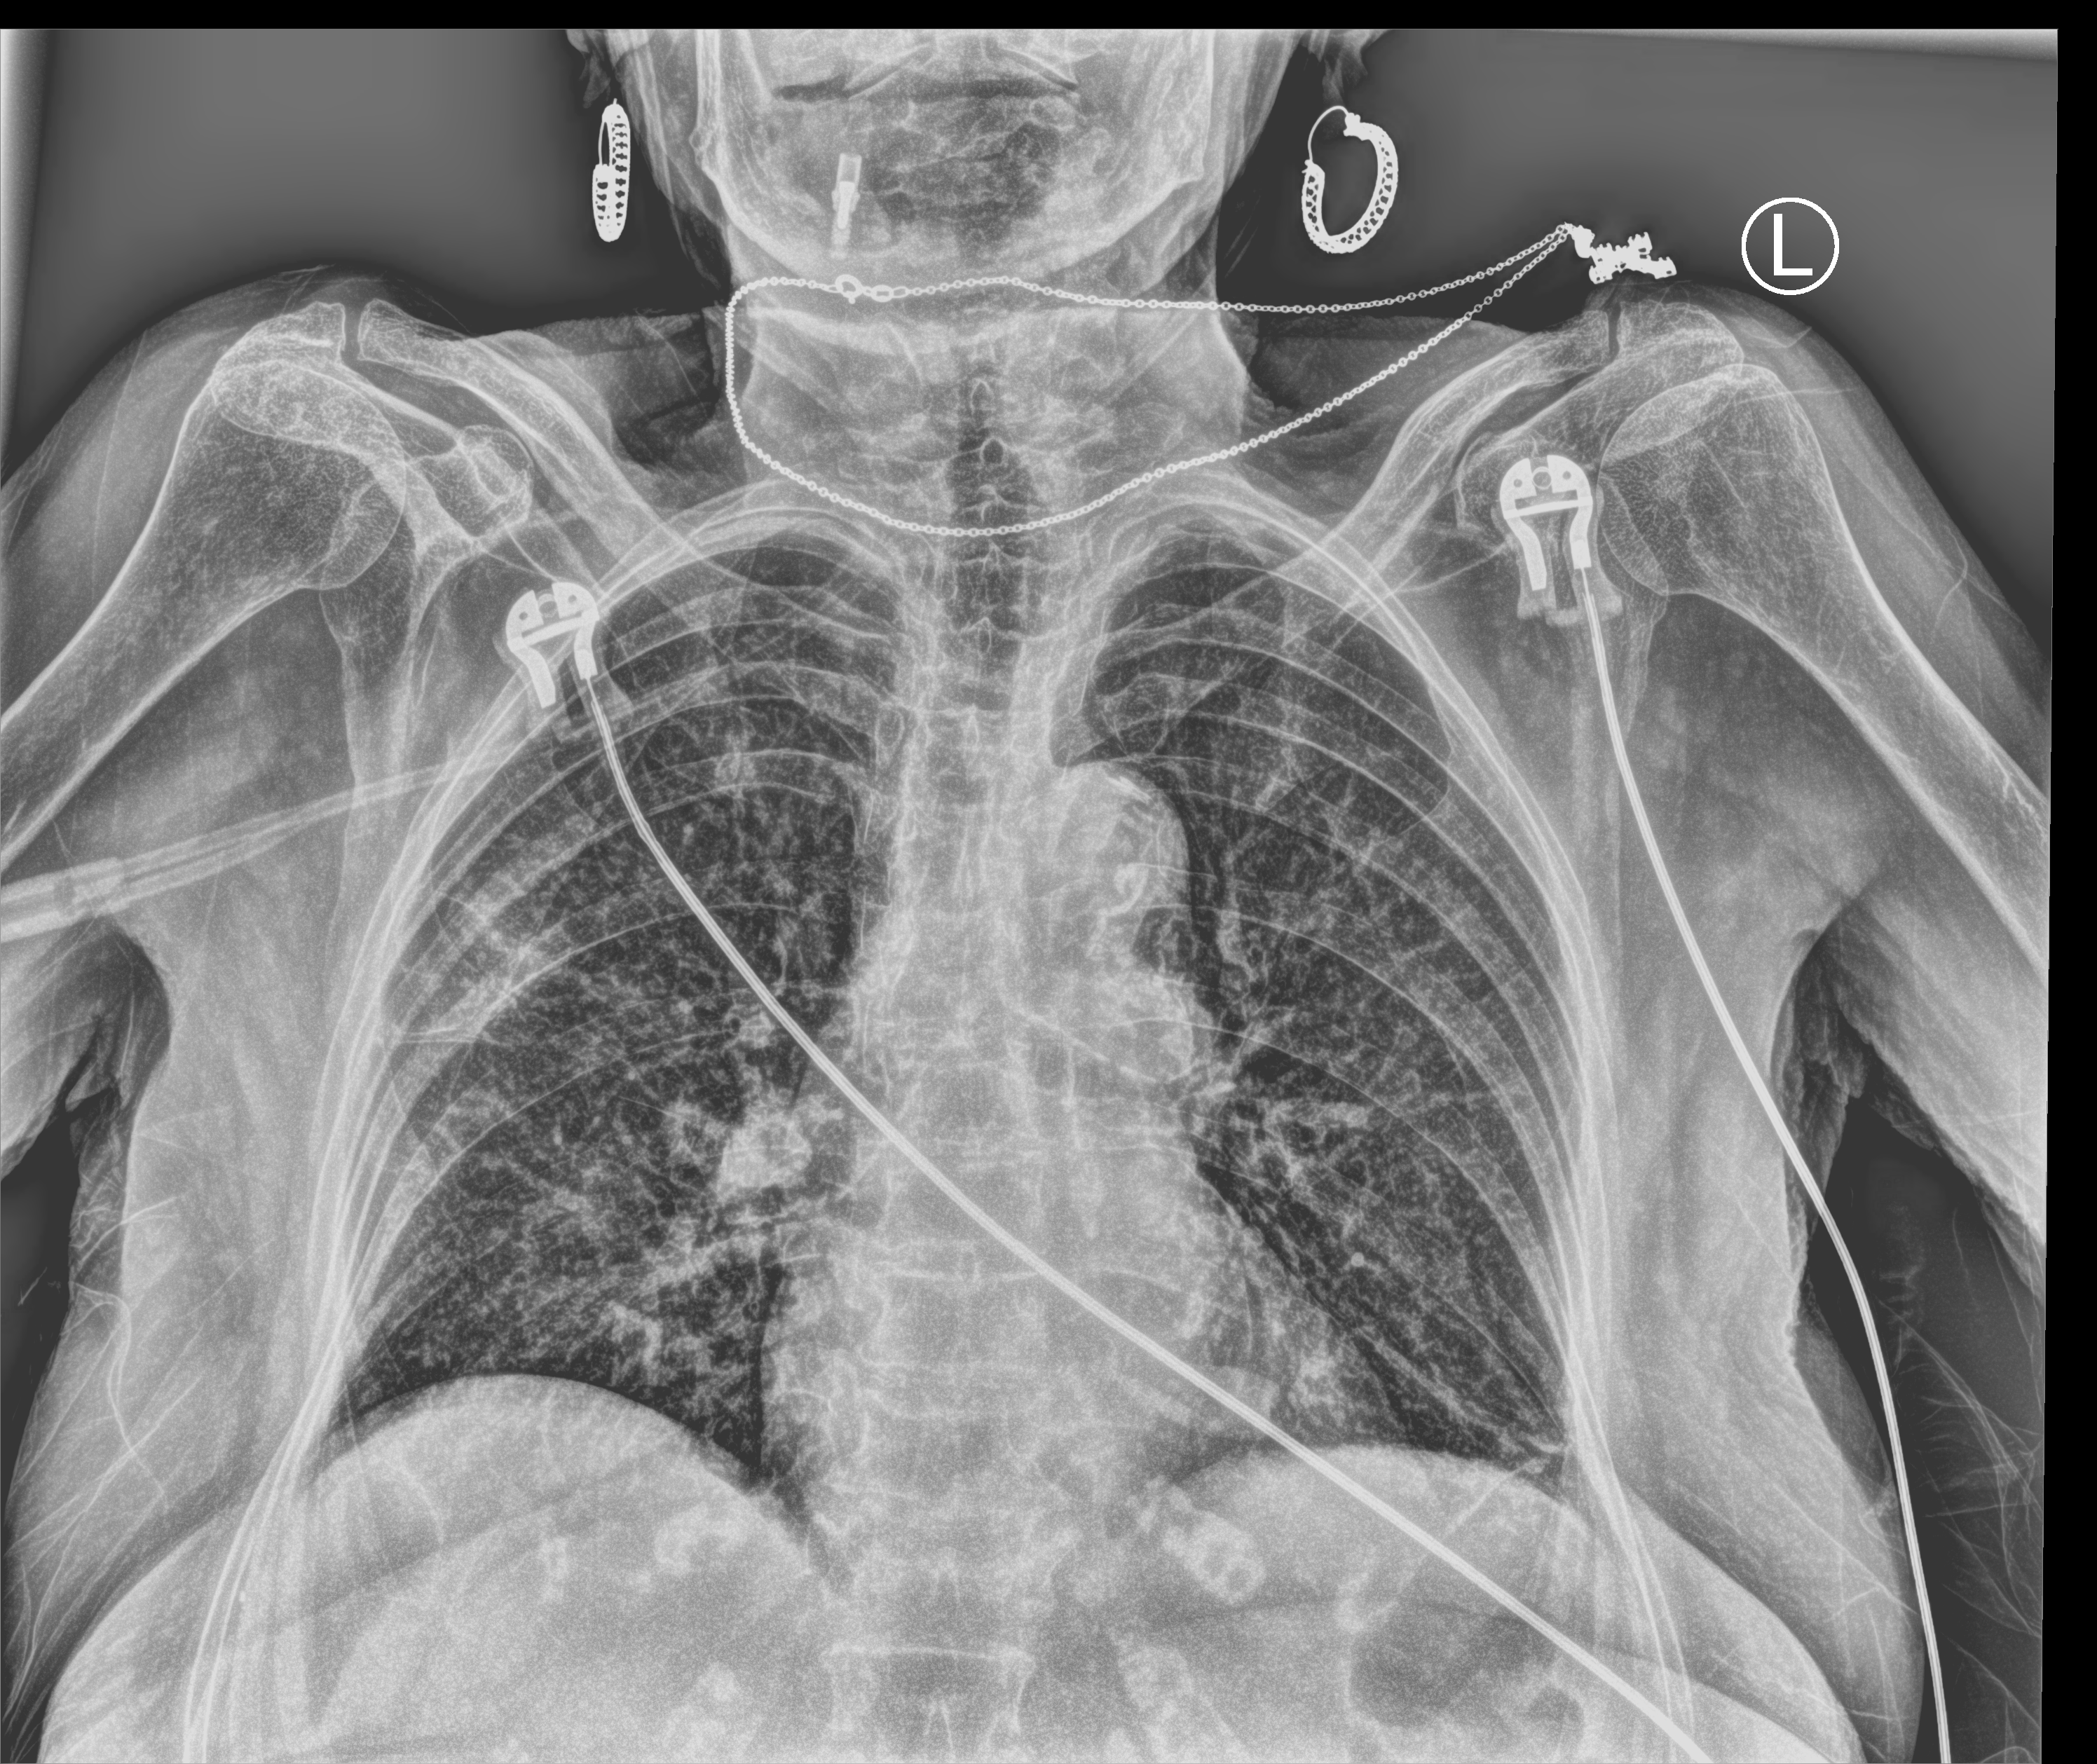
Chest X-ray (portable); anteroposterior (AP) projection. Patient hospitalised with COVID-19; female, aged 75–90 years.
From the hospital-stay record, not from the radiograph (when in the stay this image was taken is not recorded):
- length of hospital stay: 9 days
- admitted to intensive care during this hospital stay: no
- mechanically ventilated during this hospital stay: no